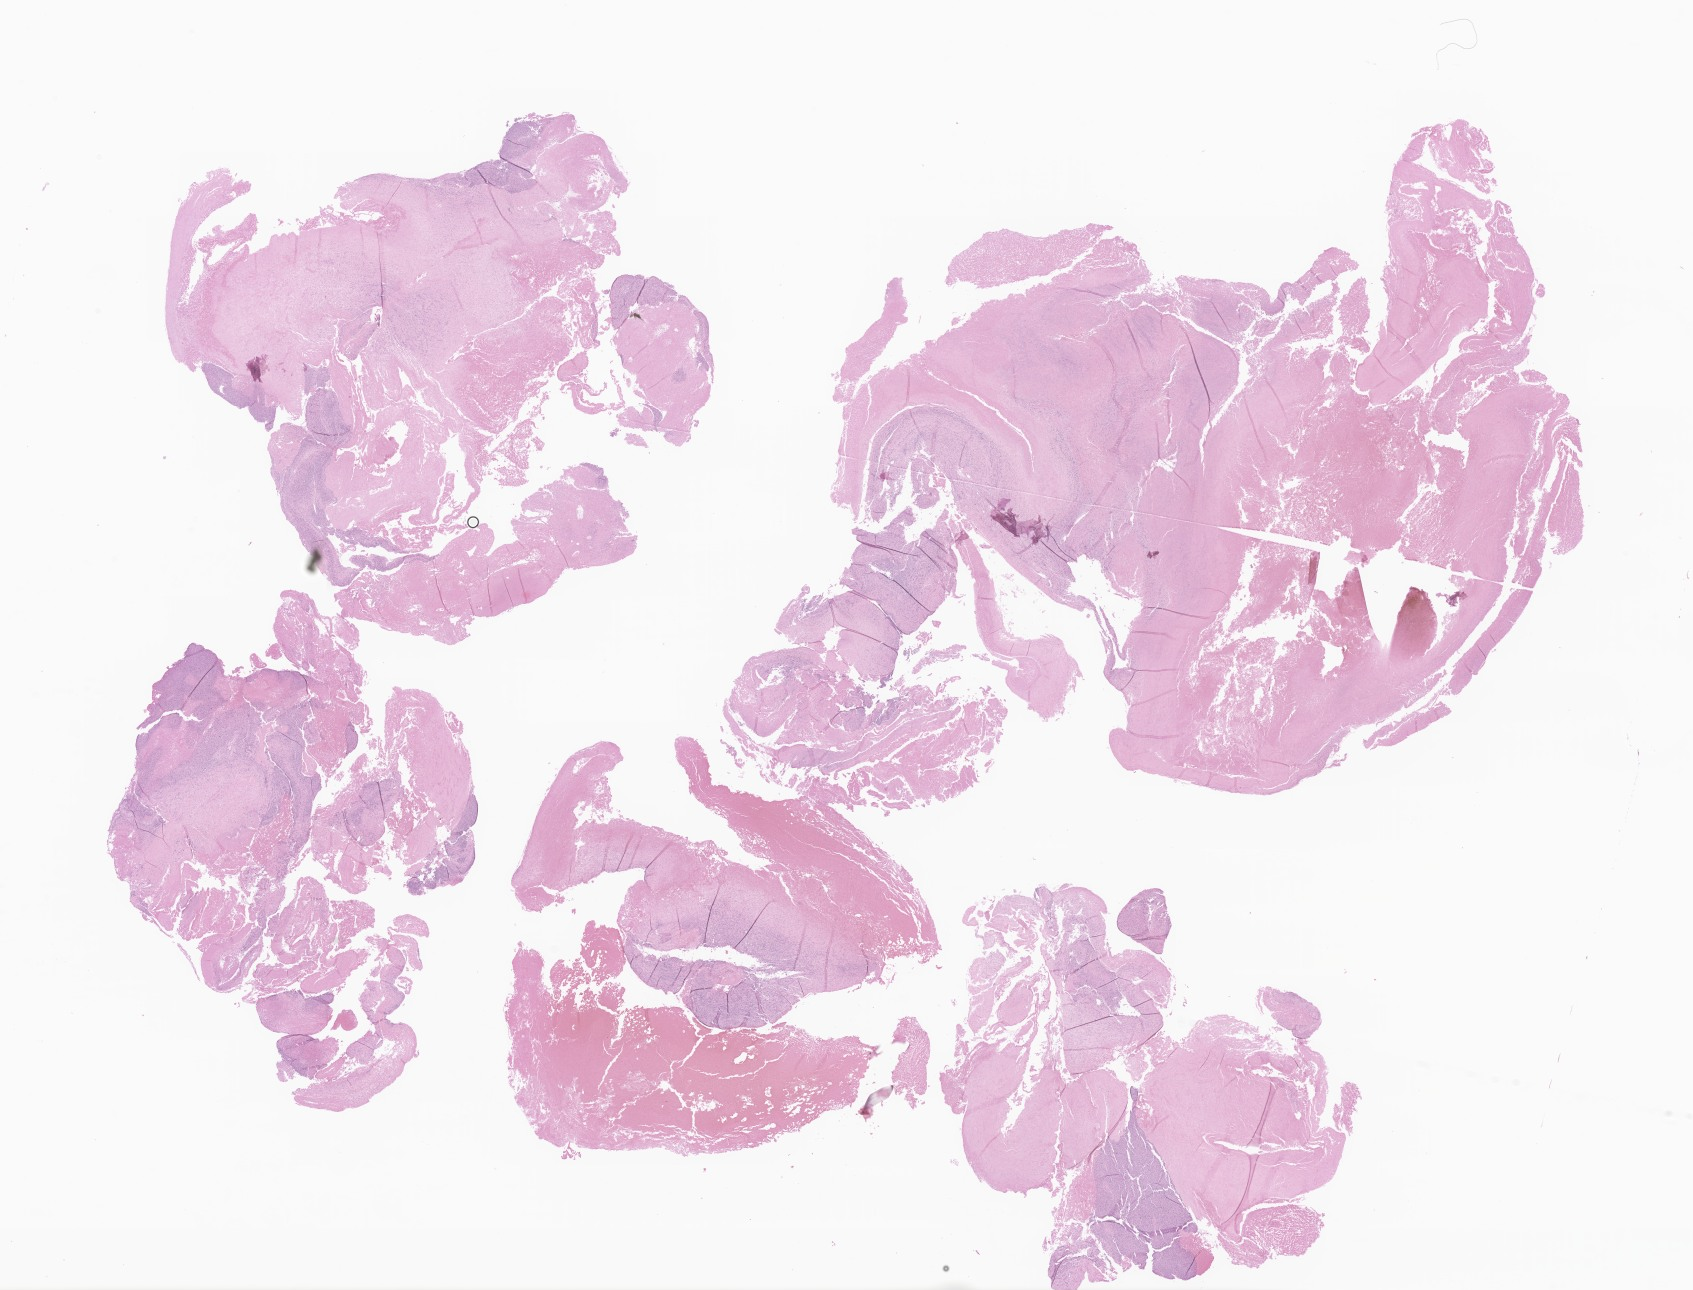
Digitized haematoxylin and eosin-stained section of tumor tissue from the soft tissue of pelvis — a low-resolution overview of the entire scanned area, about 28.6 x 21.8 mm; formalin-fixed paraffin-embedded section. Patient female; age 217 months (18 years 1 month).
Diagnosis: Spindle cell sarcoma.